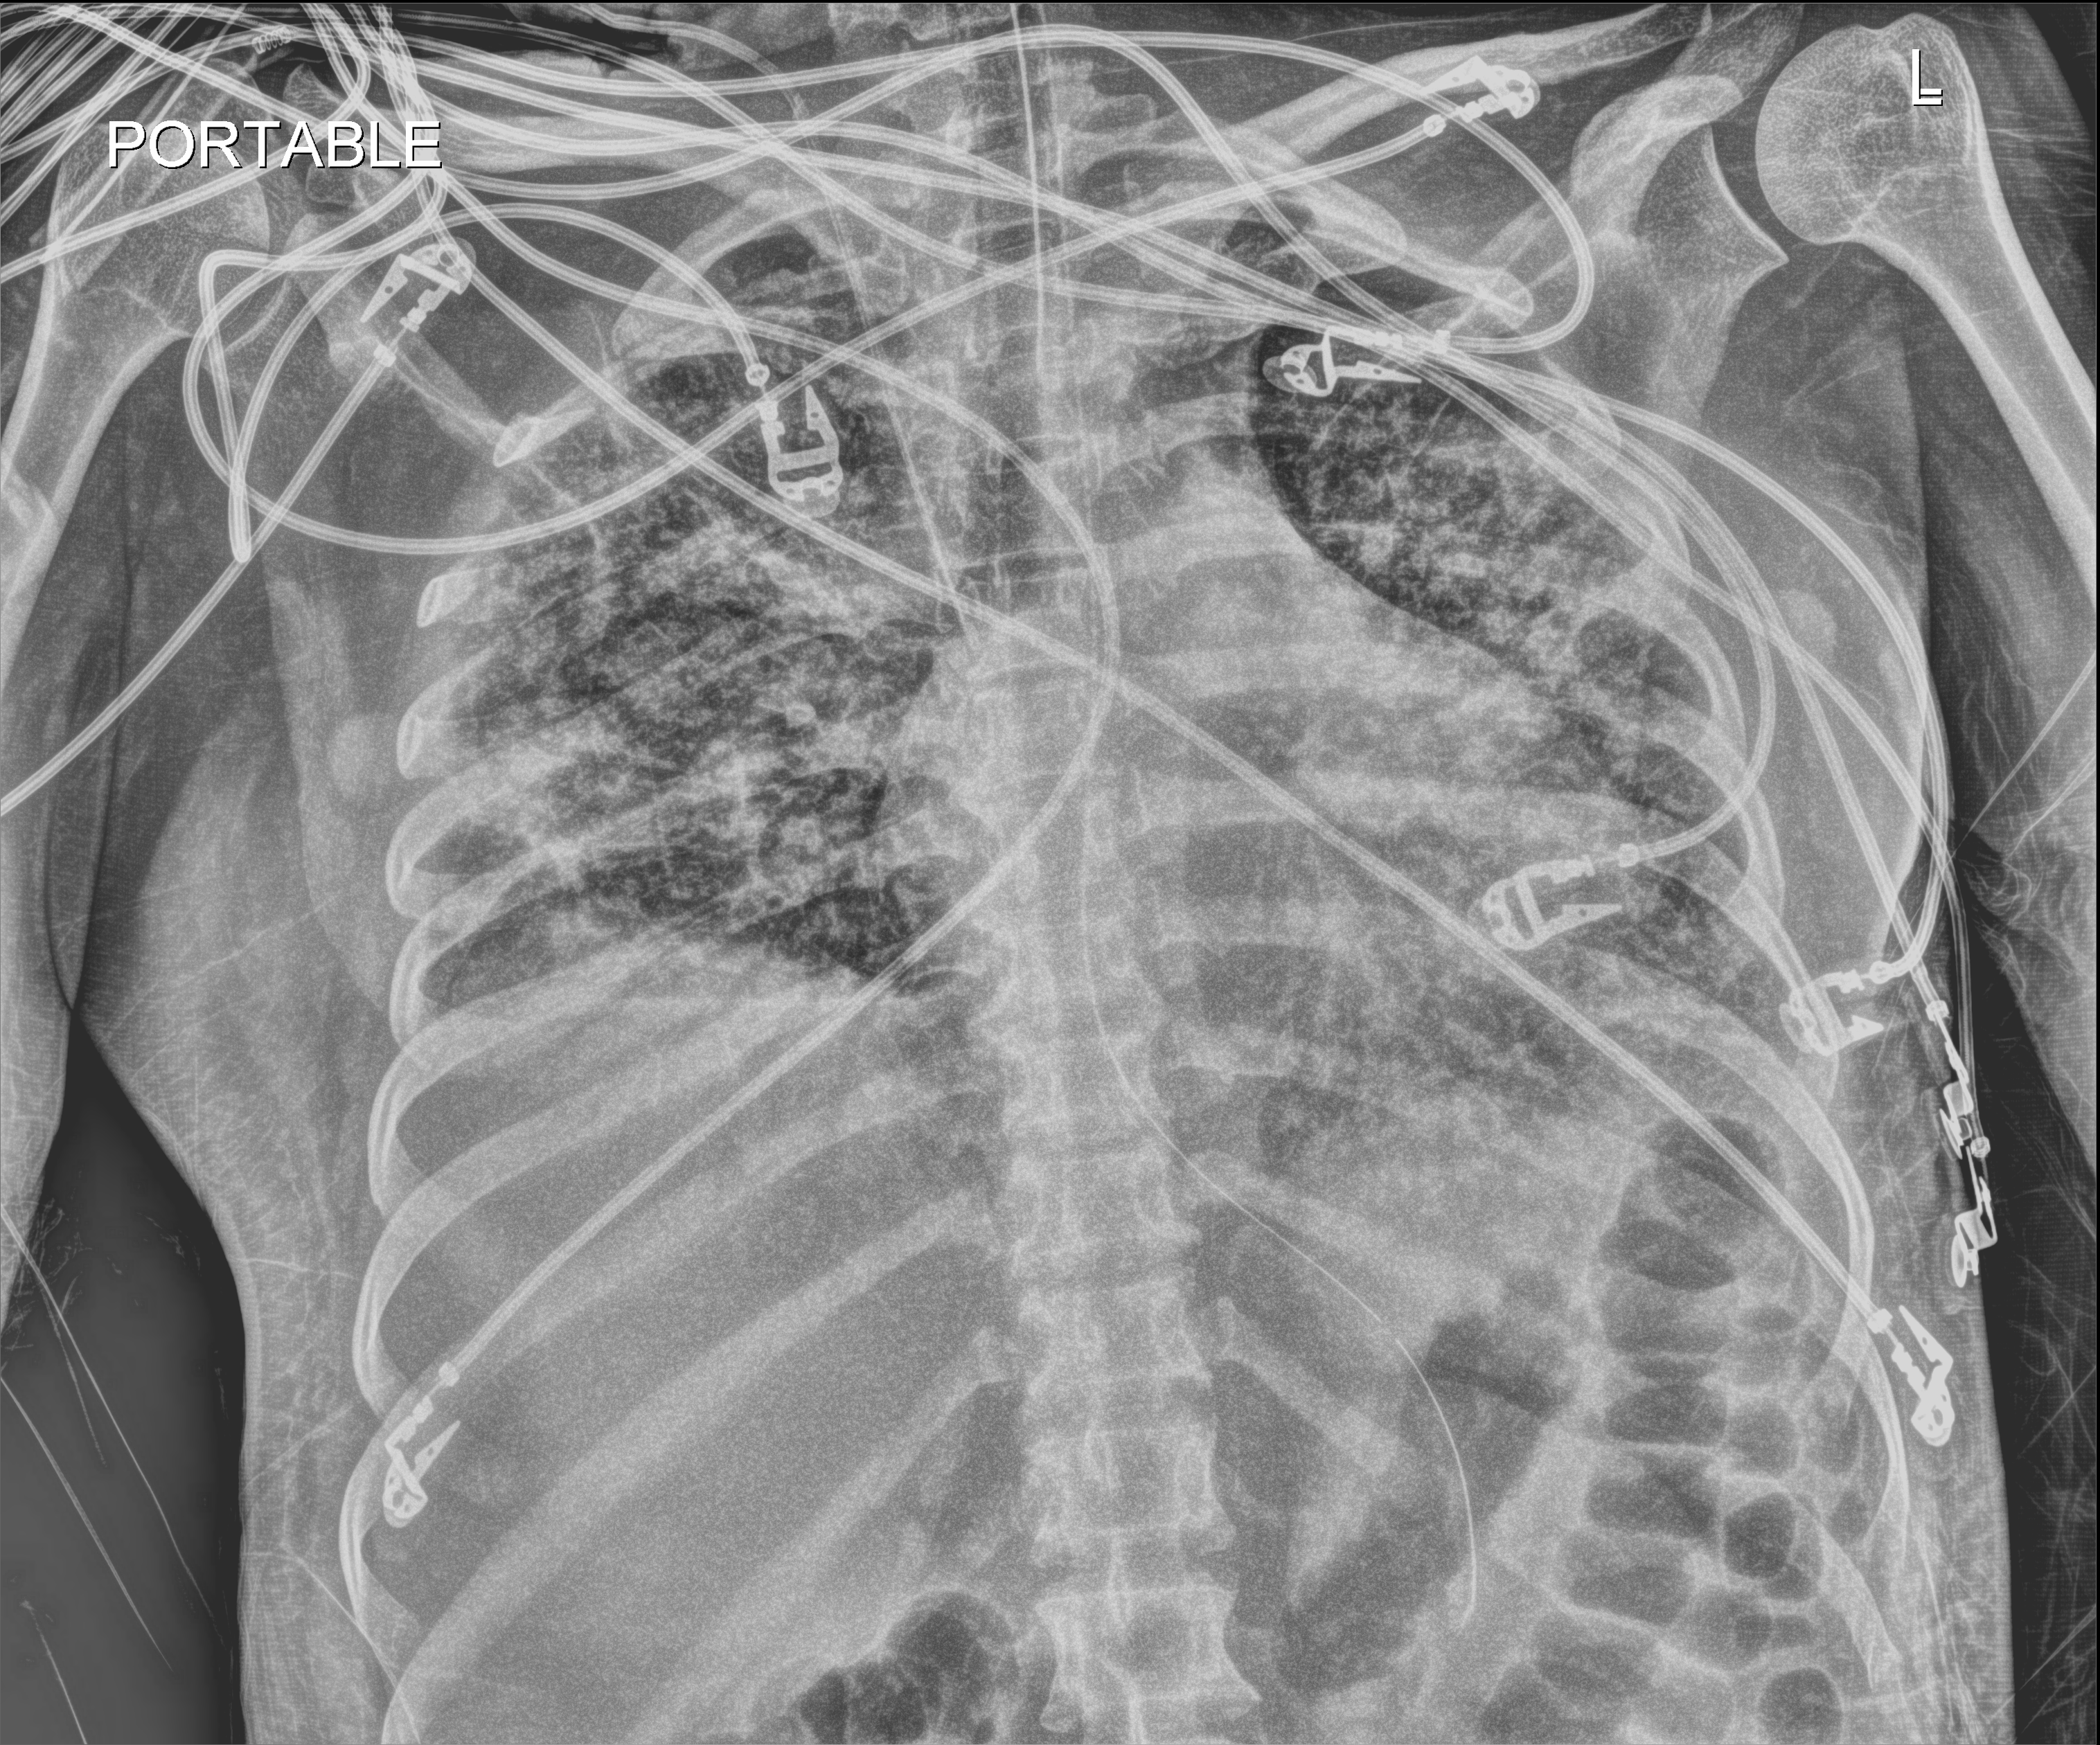
Chest X-ray (portable); anteroposterior (AP) projection. Female patient hospitalised with COVID-19, age 18–59 years.
From the hospital-stay record, not from the radiograph (when in the stay this image was taken is not recorded): mechanically ventilated during this hospital stay: yes.